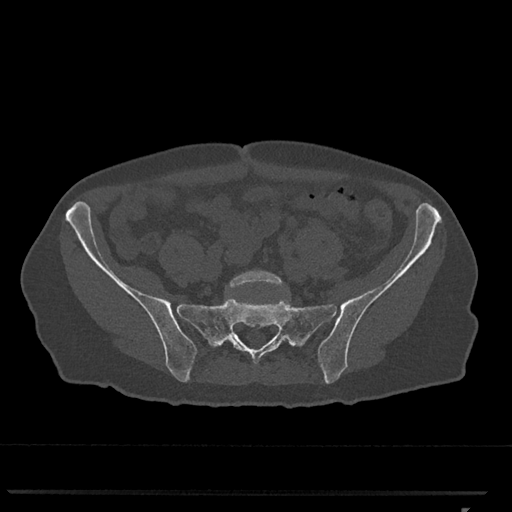
CT including the spine, one axial slice. Position 109 of 793 along the scan axis. Reconstruction kernel Br40s/3. Bone window (W 1800 / L 400 HU). 0.5 mm slice thickness. 512 × 512 image matrix, field of view 380 × 380 mm. Female patient, age 62 years. From the clinical record (not read from this slice): primary cancer: renal.
Outlined on this slice (semi-automatically segmented with operator editing):
- L5 vertebra: bounding box [x1, y1, x2, y2] px = [228, 270, 284, 289]